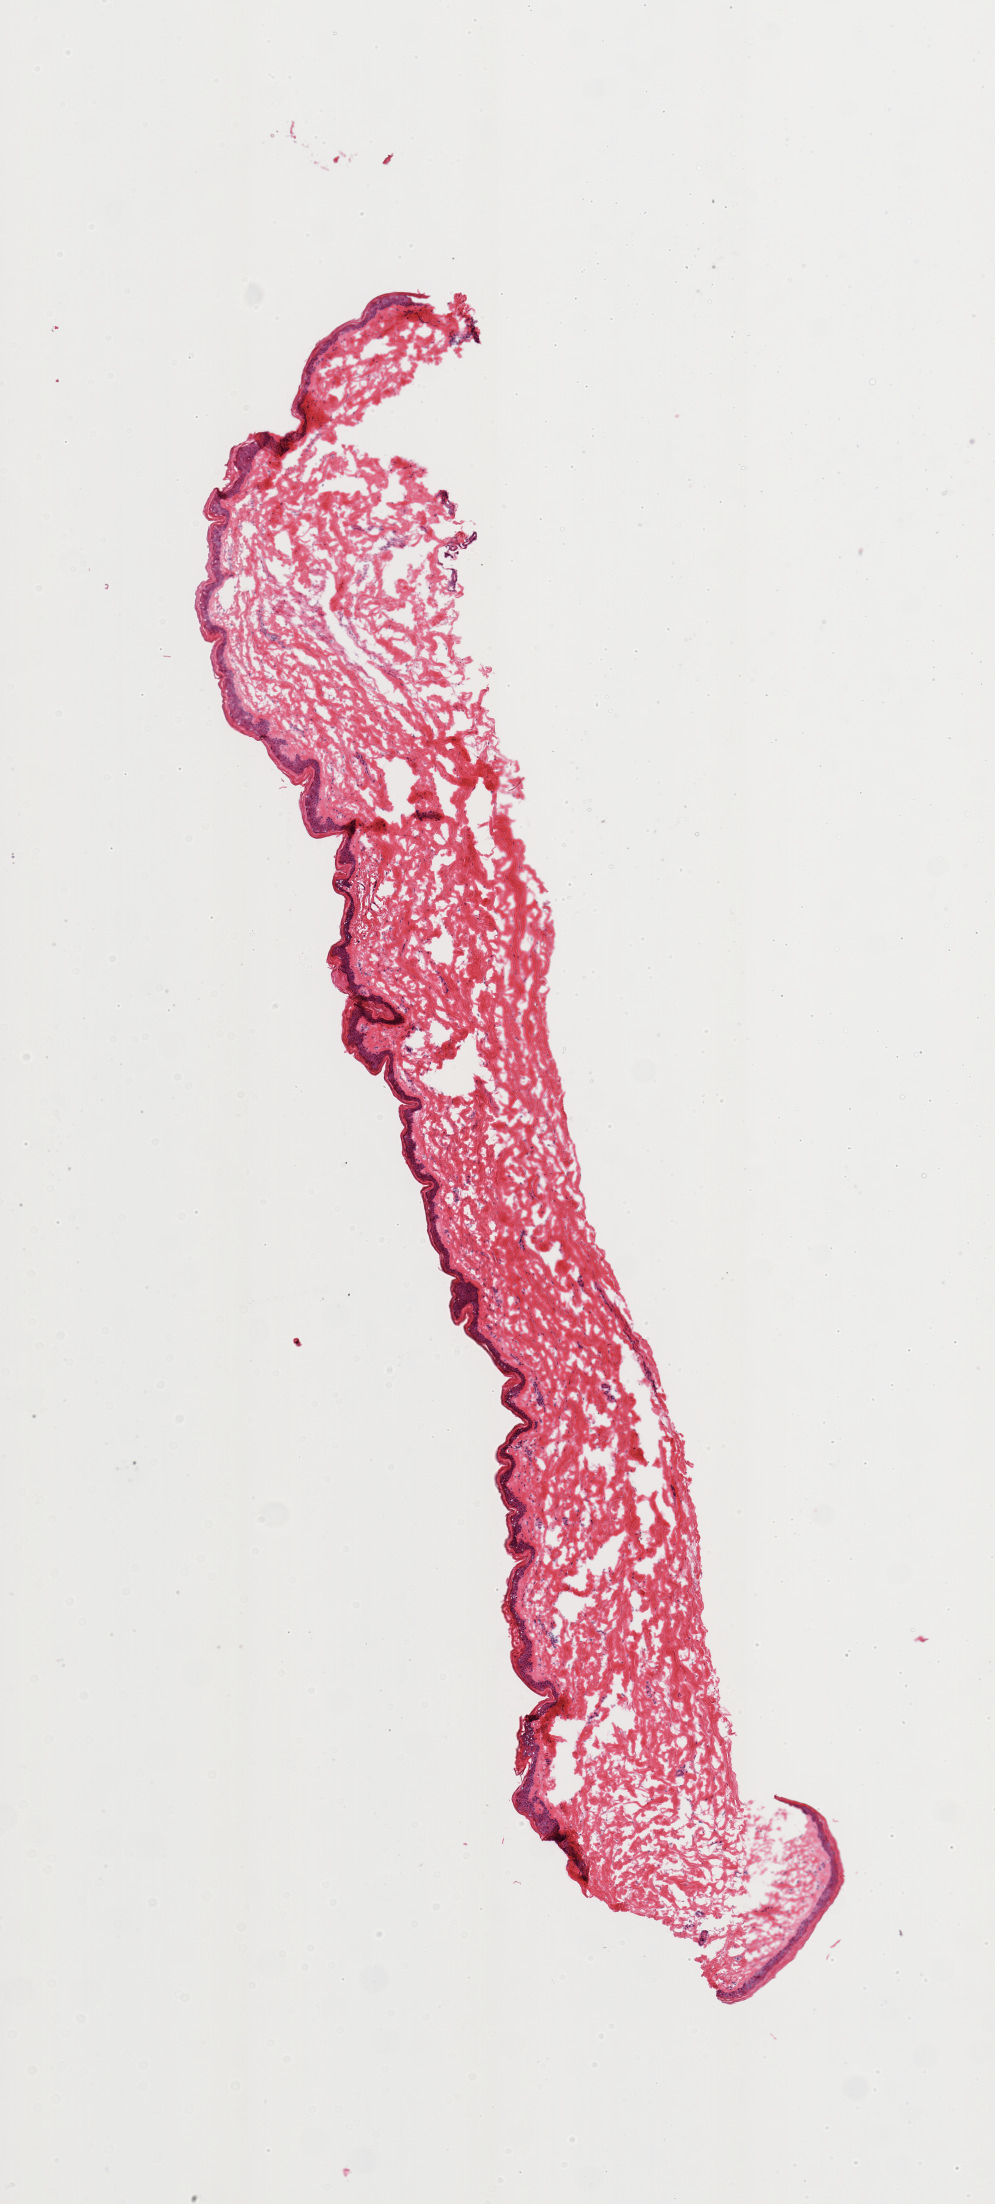
Hematoxylin and eosin (H&E) whole-slide image, shown as a low-resolution overview of the whole scanned area (about 3.9 x 8.7 mm, slide scanned at 20x), frozen section (dry ice), sampled site (target tissue): skin of lower leg, tissue donor sample.
Reviewer comment on this tissue sample: 1 piece.